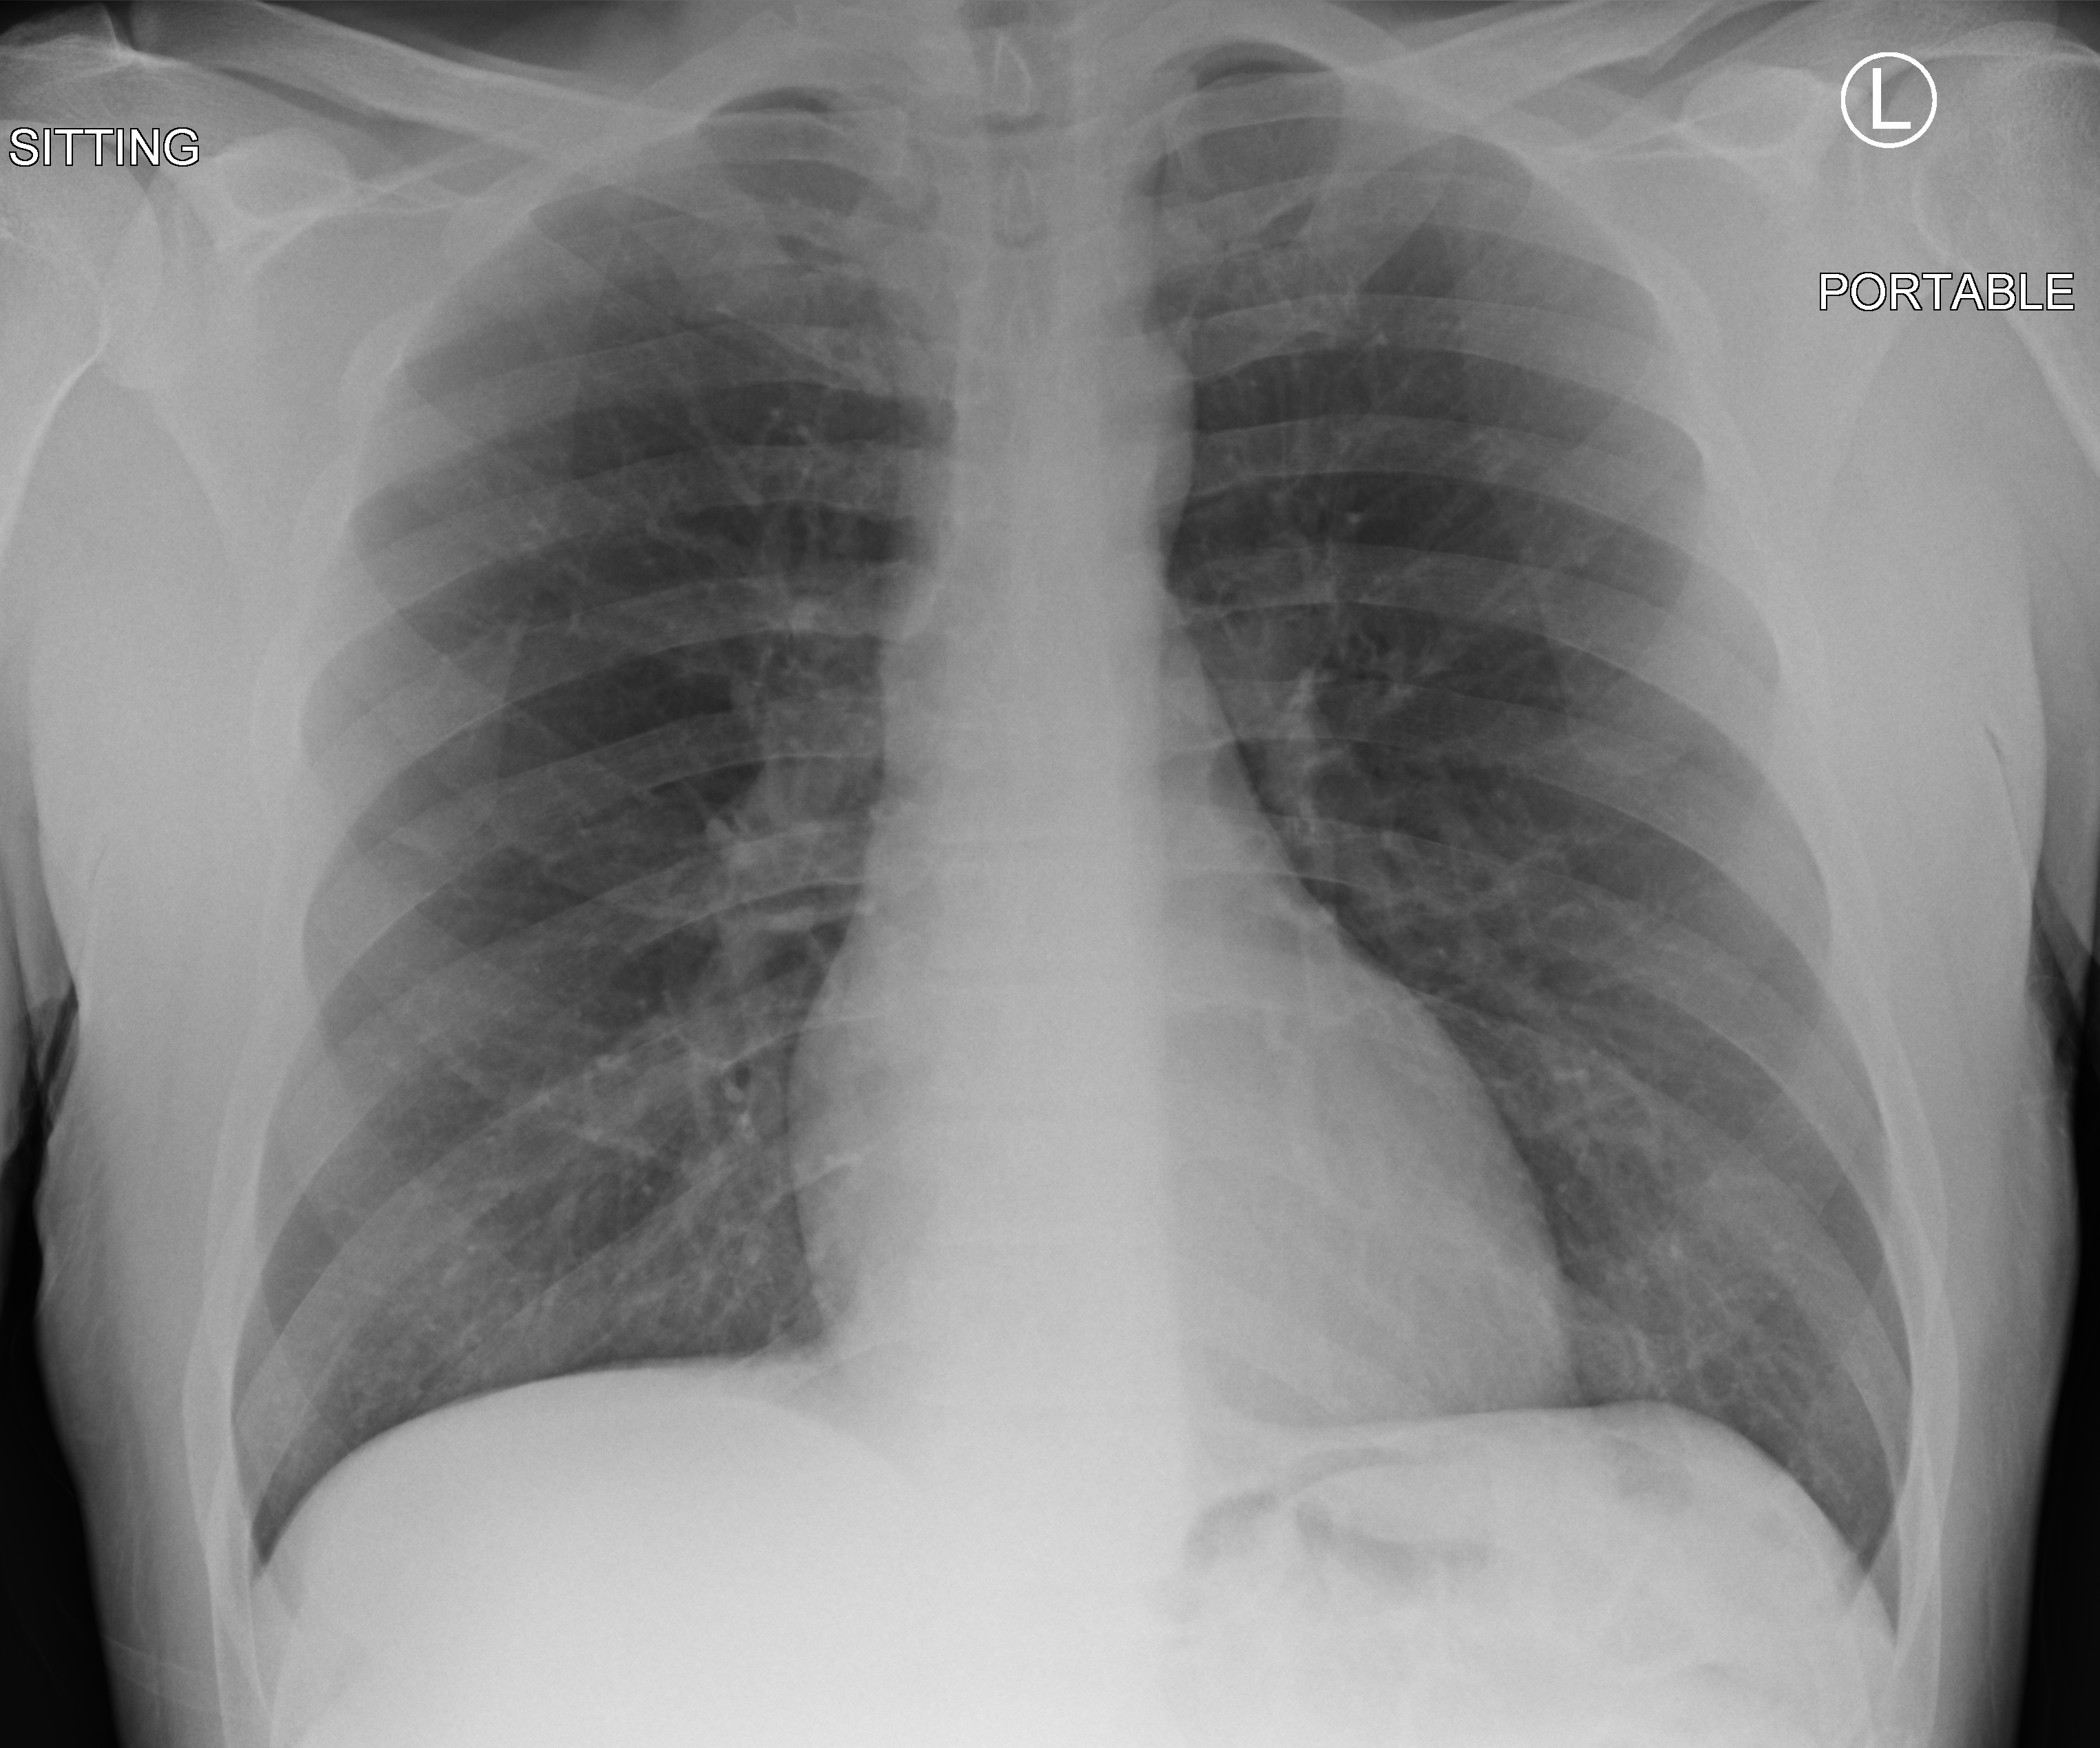
Bedside chest radiograph (computed radiography); anteroposterior (AP) projection. Patient hospitalised with COVID-19; male, aged 18–59 years.
From the hospital-stay record, not from the radiograph (when in the stay this image was taken is not recorded):
- mechanically ventilated during this hospital stay: no
- COPD (admission record): no